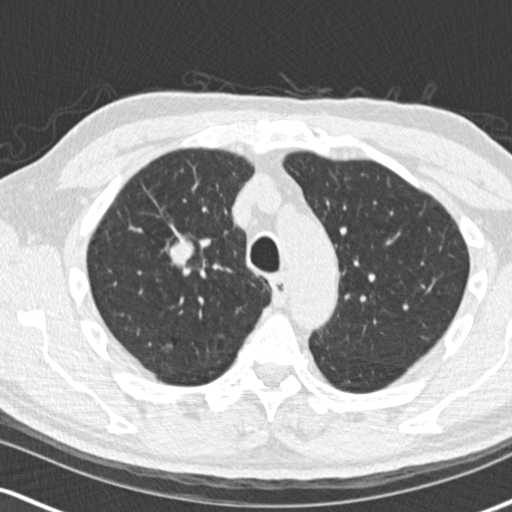
Low-dose screening chest CT, one axial slice. Slice 115 of 170 in the series (ordered by position). Reconstruction kernel B30f. 120 kVp. Lung window (W 1500 / L -600 HU). 2 mm slice thickness. 512 × 512 image matrix, field of view 320 × 320 mm.
Annotated regions visible in this slice (manually delineated by an expert):
- lesion 1 (tumor, upper lobe of right lung): bounding box <169,242,194,267> (left, top, right, bottom; pixels)